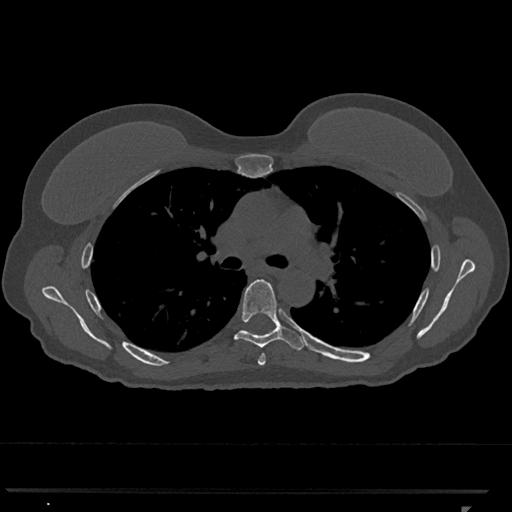
CT including the spine, one axial slice. Reconstruction kernel Br40s/3. 120 kVp. Bone window (W 1800 / L 400 HU). 0.5 mm slice thickness. 512 × 512 image matrix, field of view 380 × 380 mm. Female patient, age 62 years. From the clinical record (not read from this slice): primary cancer: renal.
Structures marked on this image (semi-automatically segmented with operator editing):
- T5 vertebra: bounding box [x1, y1, x2, y2] px = [258, 354, 266, 366]
- T6 vertebra: [224, 279, 305, 350]